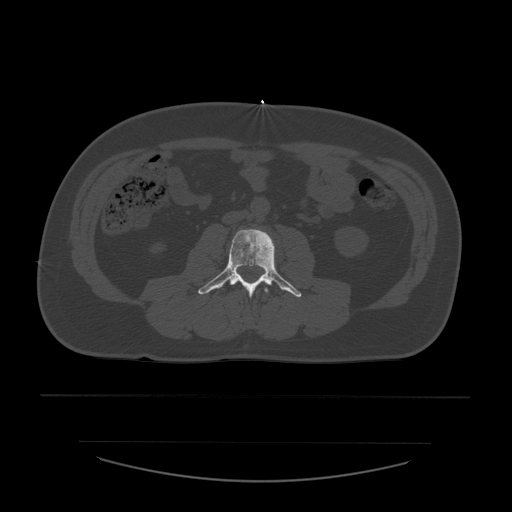
CT including the spine, one axial slice; position 176 of 532 along the scan axis; 120 kVp; bone window (W 1800 / L 400 HU); 512 × 512 image matrix, field of view 441 × 441 mm. Patient age 44 years. Case-level facts recorded for this patient, not image findings: primary cancer: soft tissue sarcoma.
Structures marked on this image (semi-automatically segmented with operator editing):
- L2 vertebra: bounding box <264,288,269,294> (left, top, right, bottom; pixels)
- L3 vertebra: <198,229,302,298>